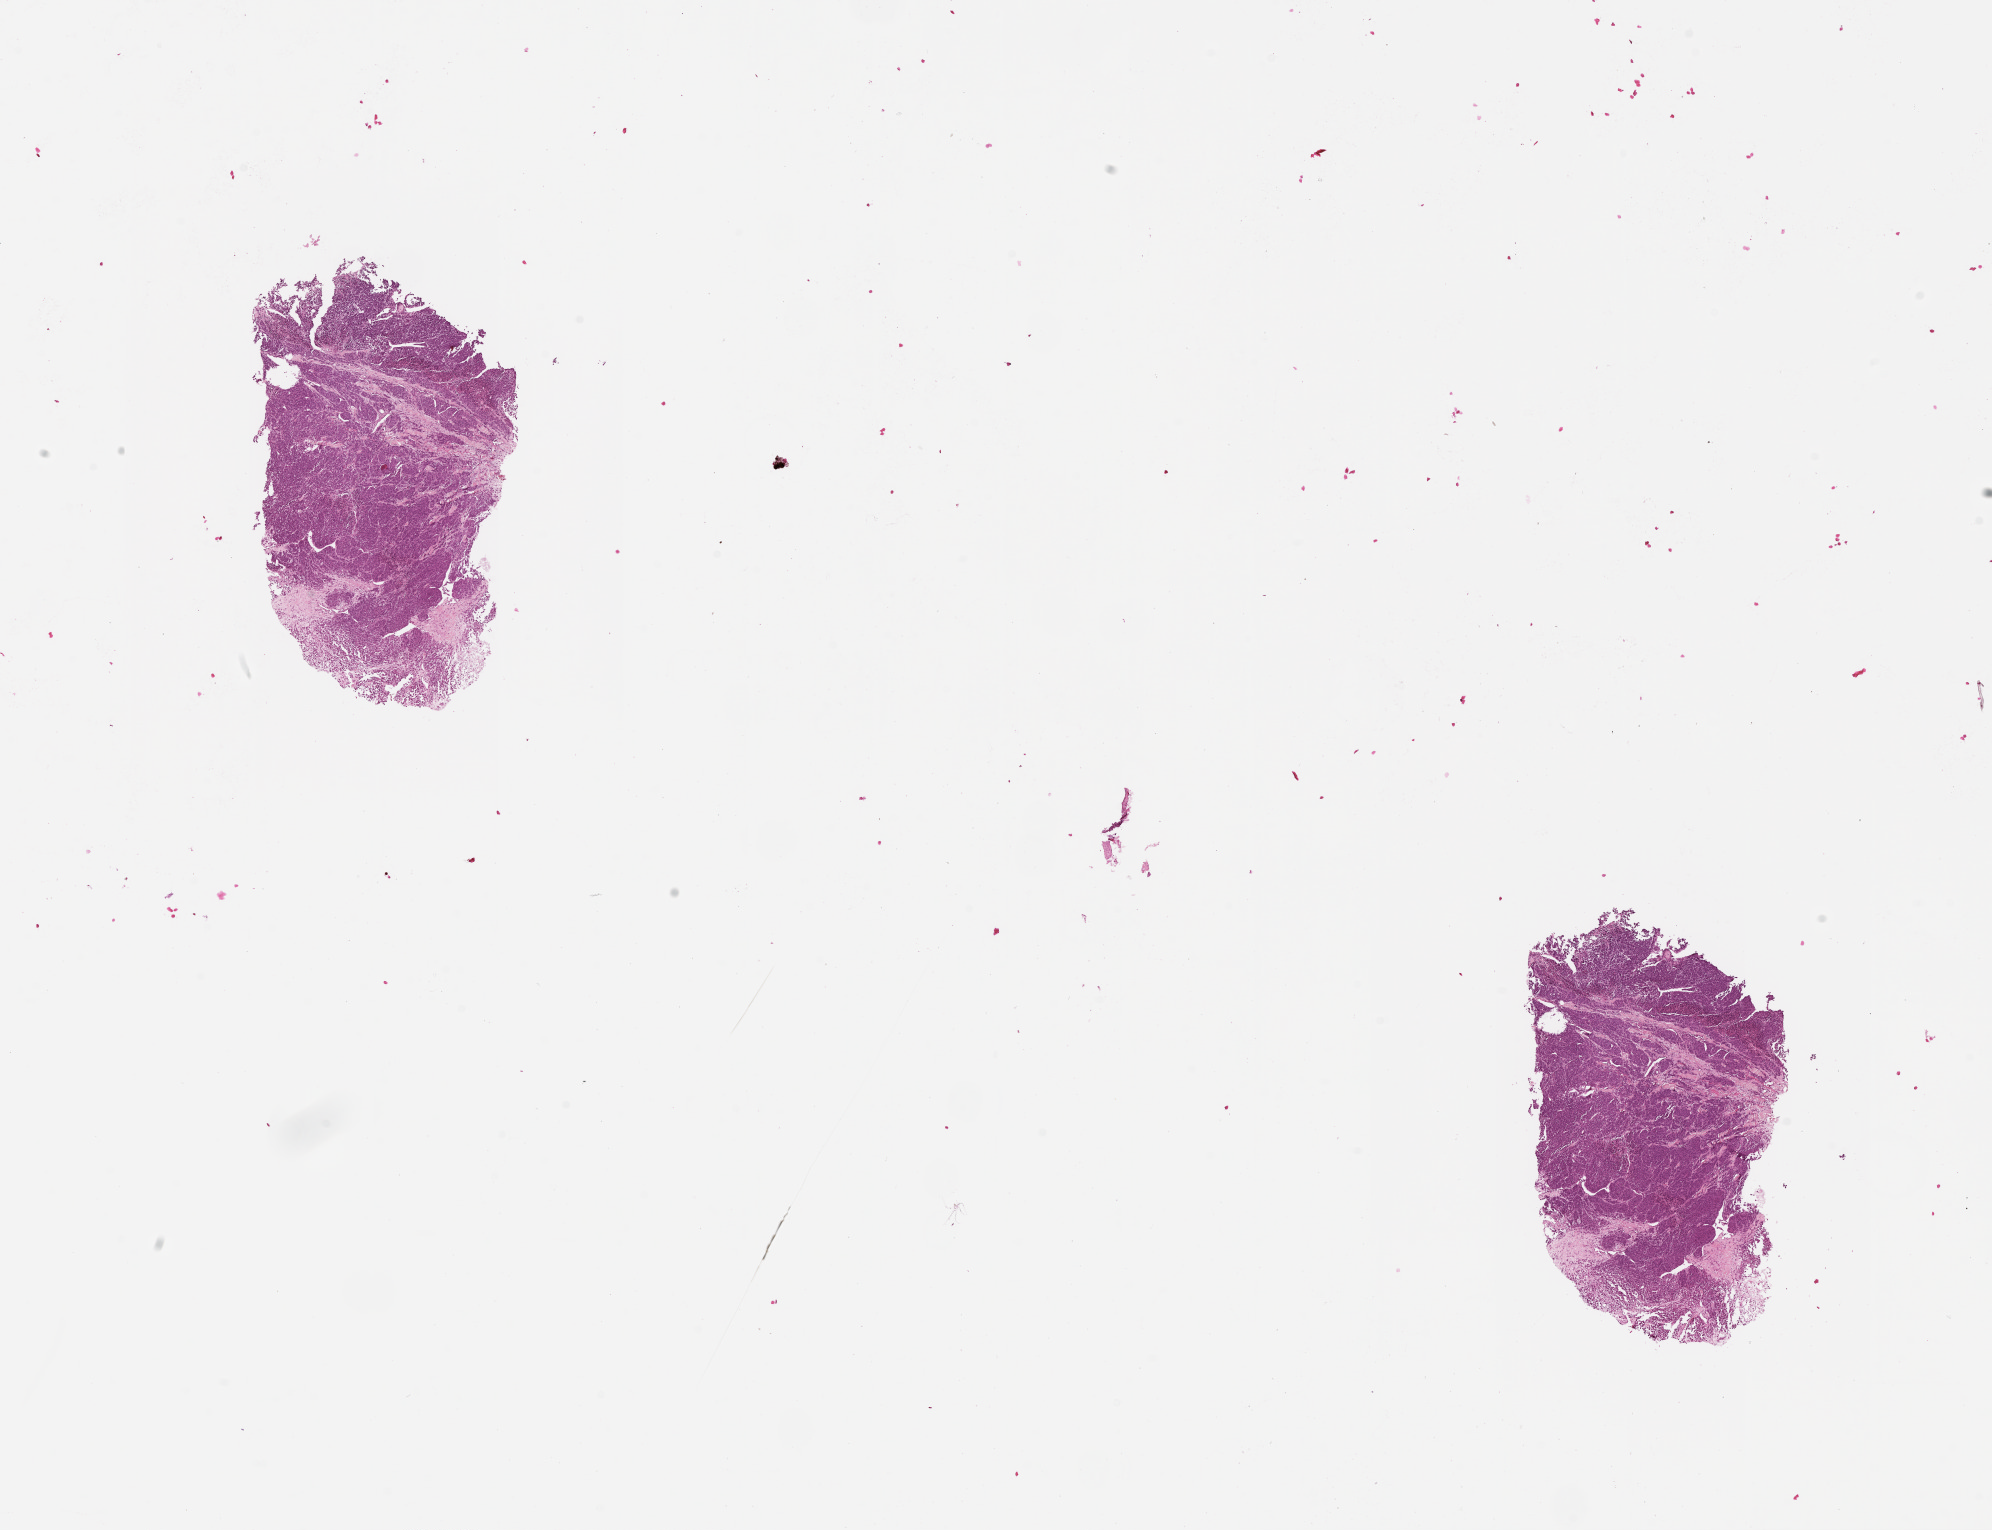
Whole-slide histology image, Hematoxylin and eosin (H&E) stained, shown as a low-resolution overview of the whole scanned area (about 16.0 x 12.3 mm, slide scanned at 20x). Tumour tissue sample, sampled site: lymph node. Male, 57 y/o. Pathologist review of this section (percent, as recorded): tumour nuclei 80%, necrosis 0%.
This section: metastatic tumour tissue. Patient diagnosis: Malignant melanoma, NOS.